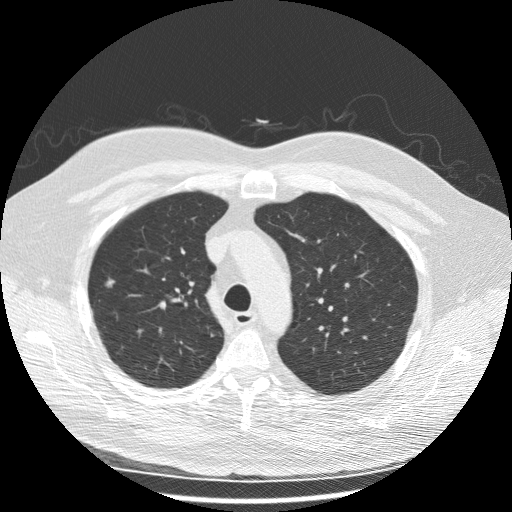
Low-dose screening chest CT, one axial slice; reconstruction kernel STANDARD; lung window (W 1500 / L -600 HU); 2.5 mm slice thickness; 512 × 512 image matrix, field of view 380 × 380 mm.
Outlined on this slice (manually delineated by an expert):
- lesion 1 (tumor, upper lobe of right lung): box from (x=105, y=278) to (x=115, y=288) px